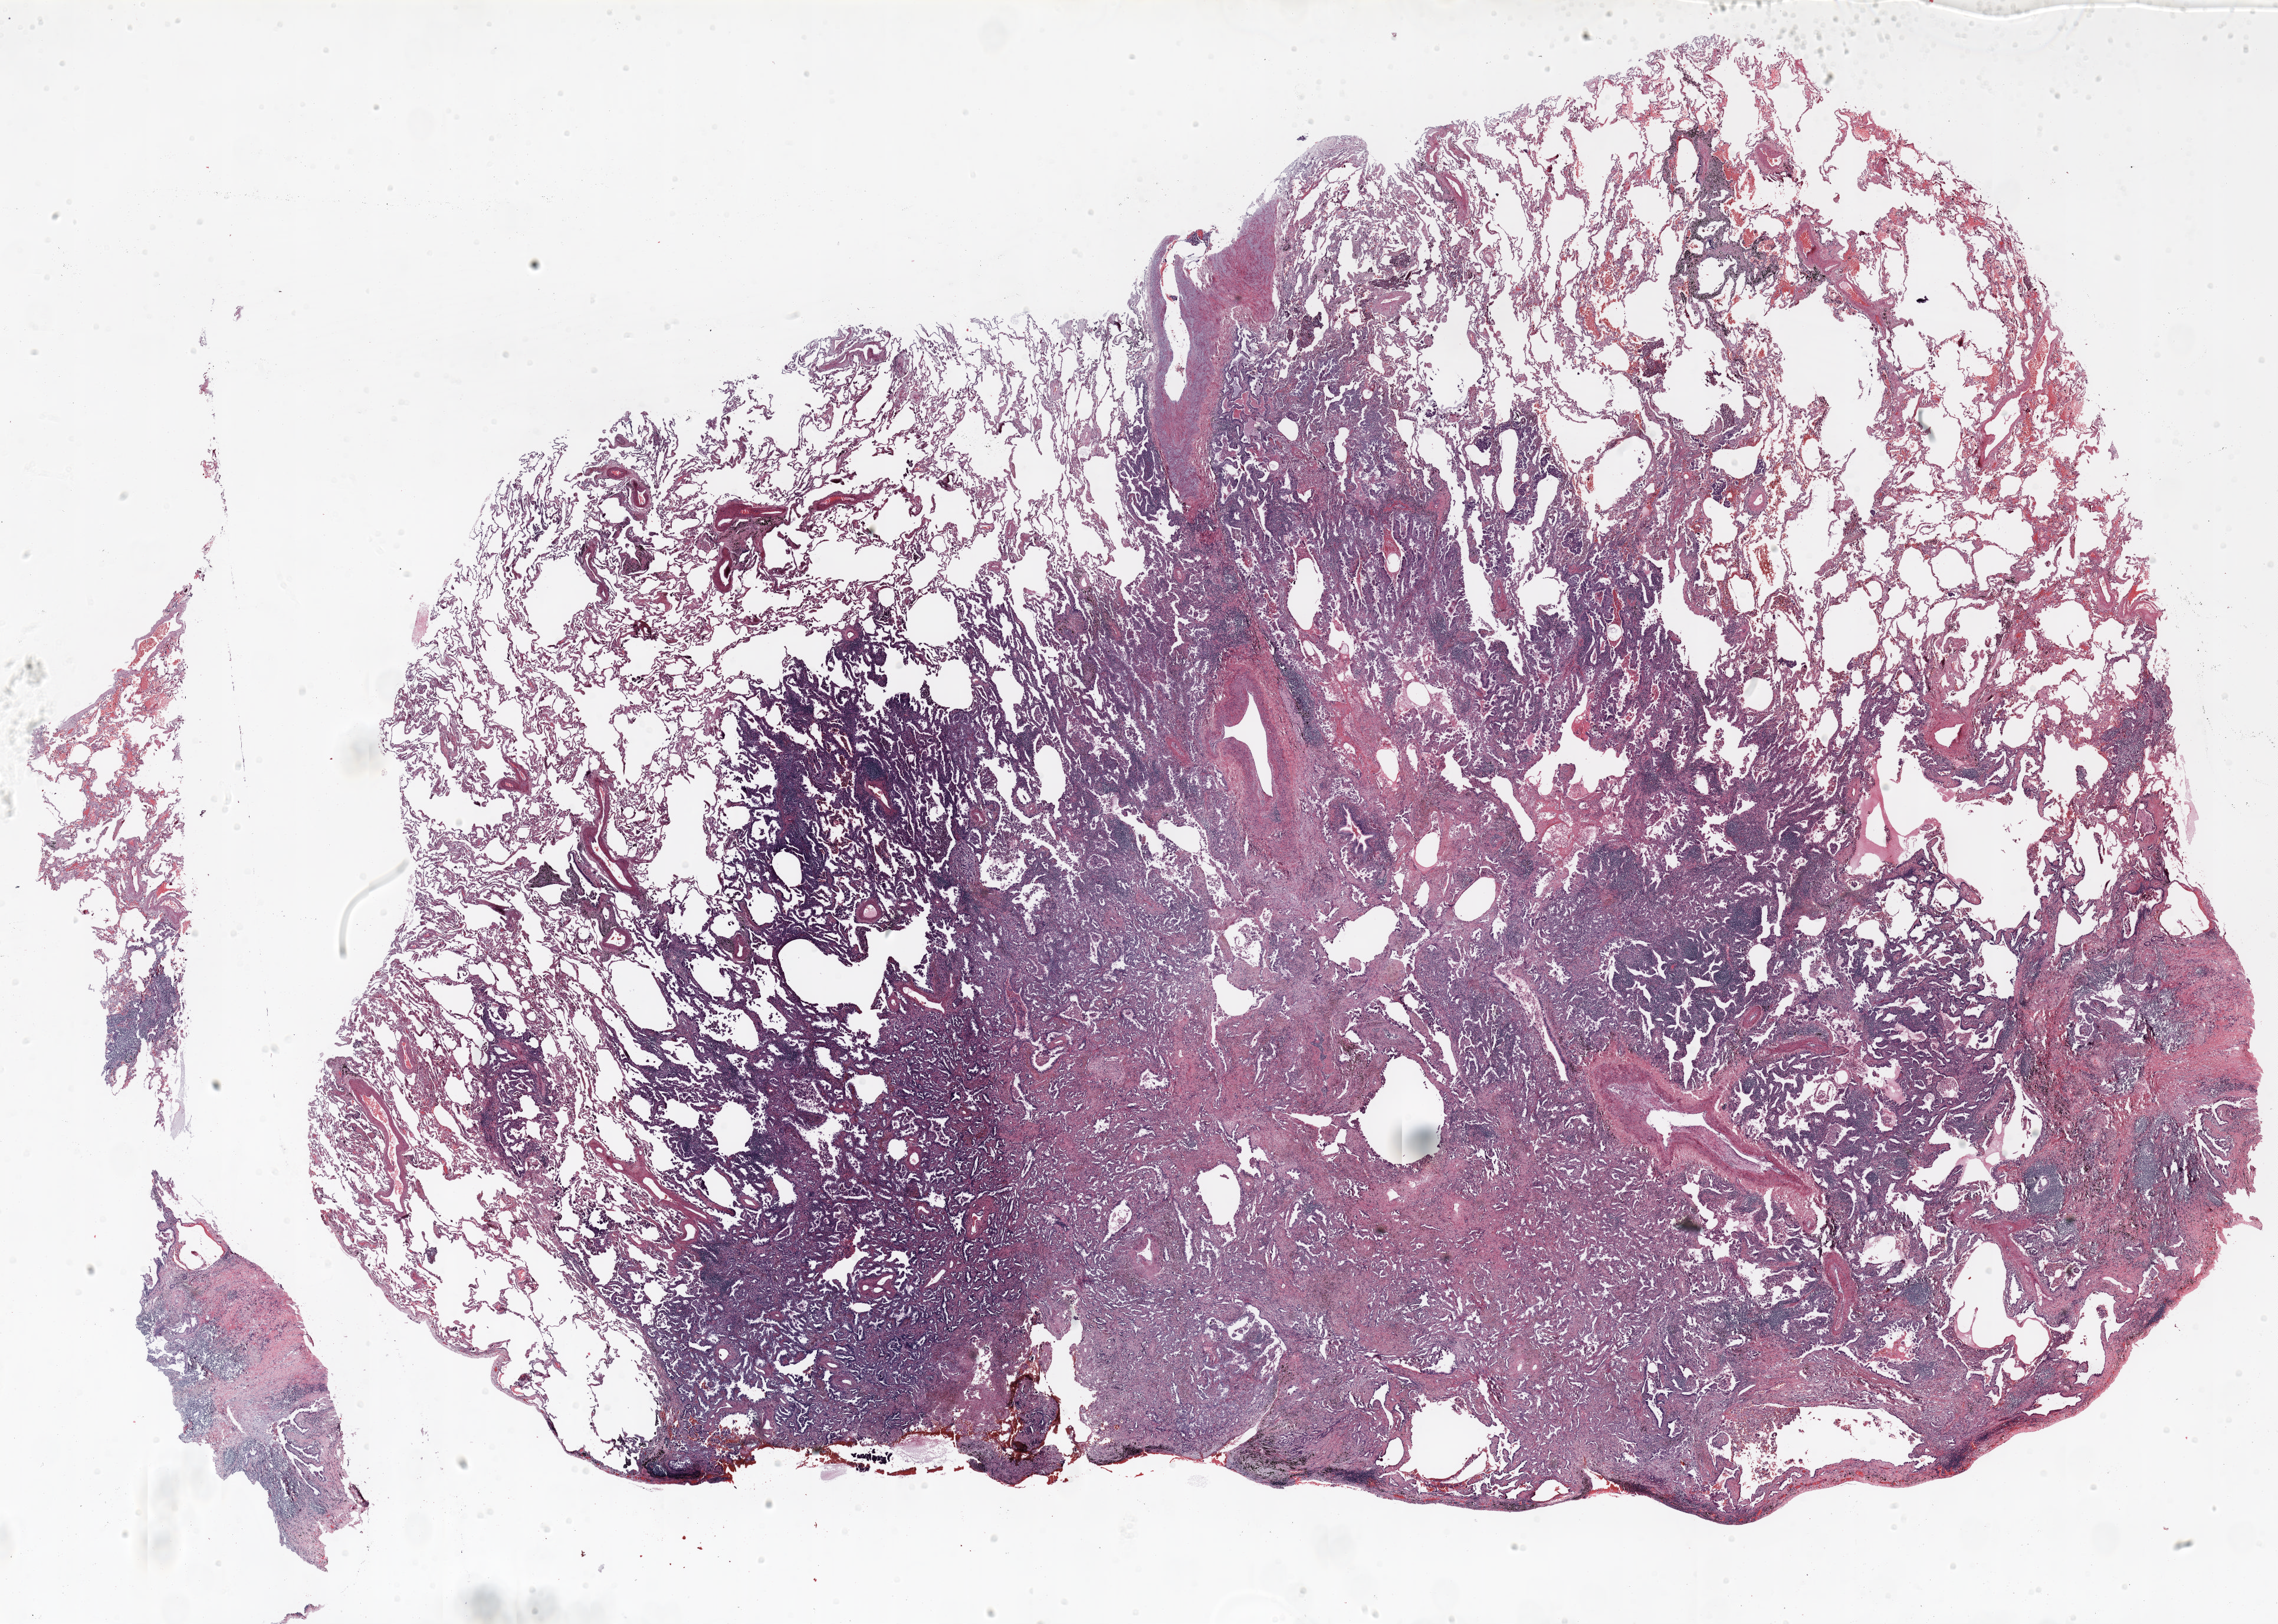
H&E whole-slide image — low-resolution overview of the scanned area, about 31.0 x 22.1 mm (acquisition: 20x scan); FFPE section; lung tissue. Male, age 72 at enrolment. Current smoker at enrolment. Grade: moderately differentiated (G2).
• stage (AJCC 6th edition): IB
• participant's lung-cancer diagnosis: Adenocarcinoma, NOS
• tumour size (pathology): 30 mm
• primary tumour location (clinical record): right upper lobe